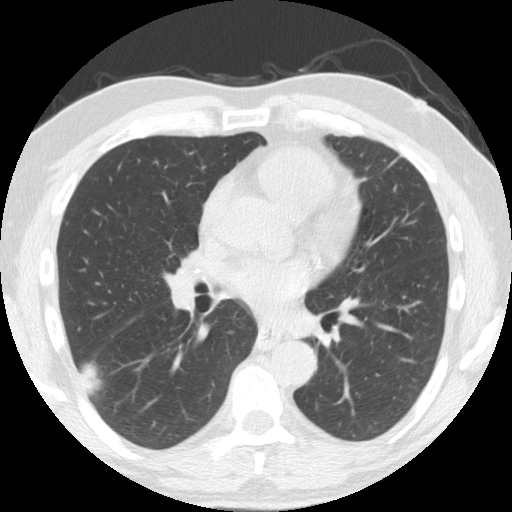
Low-dose screening chest CT, one axial slice. Position 87 of 174 along the scan axis. 120 kVp. Lung window (W 1500 / L -600 HU). 2.5 mm slice thickness. 512 × 512 image matrix, field of view 341 × 341 mm.
Annotated regions visible in this slice (expert manual segmentation):
- lesion 1 (tumor, lower lobe of right lung): bounding box [x1, y1, x2, y2] px = [80, 364, 102, 396]